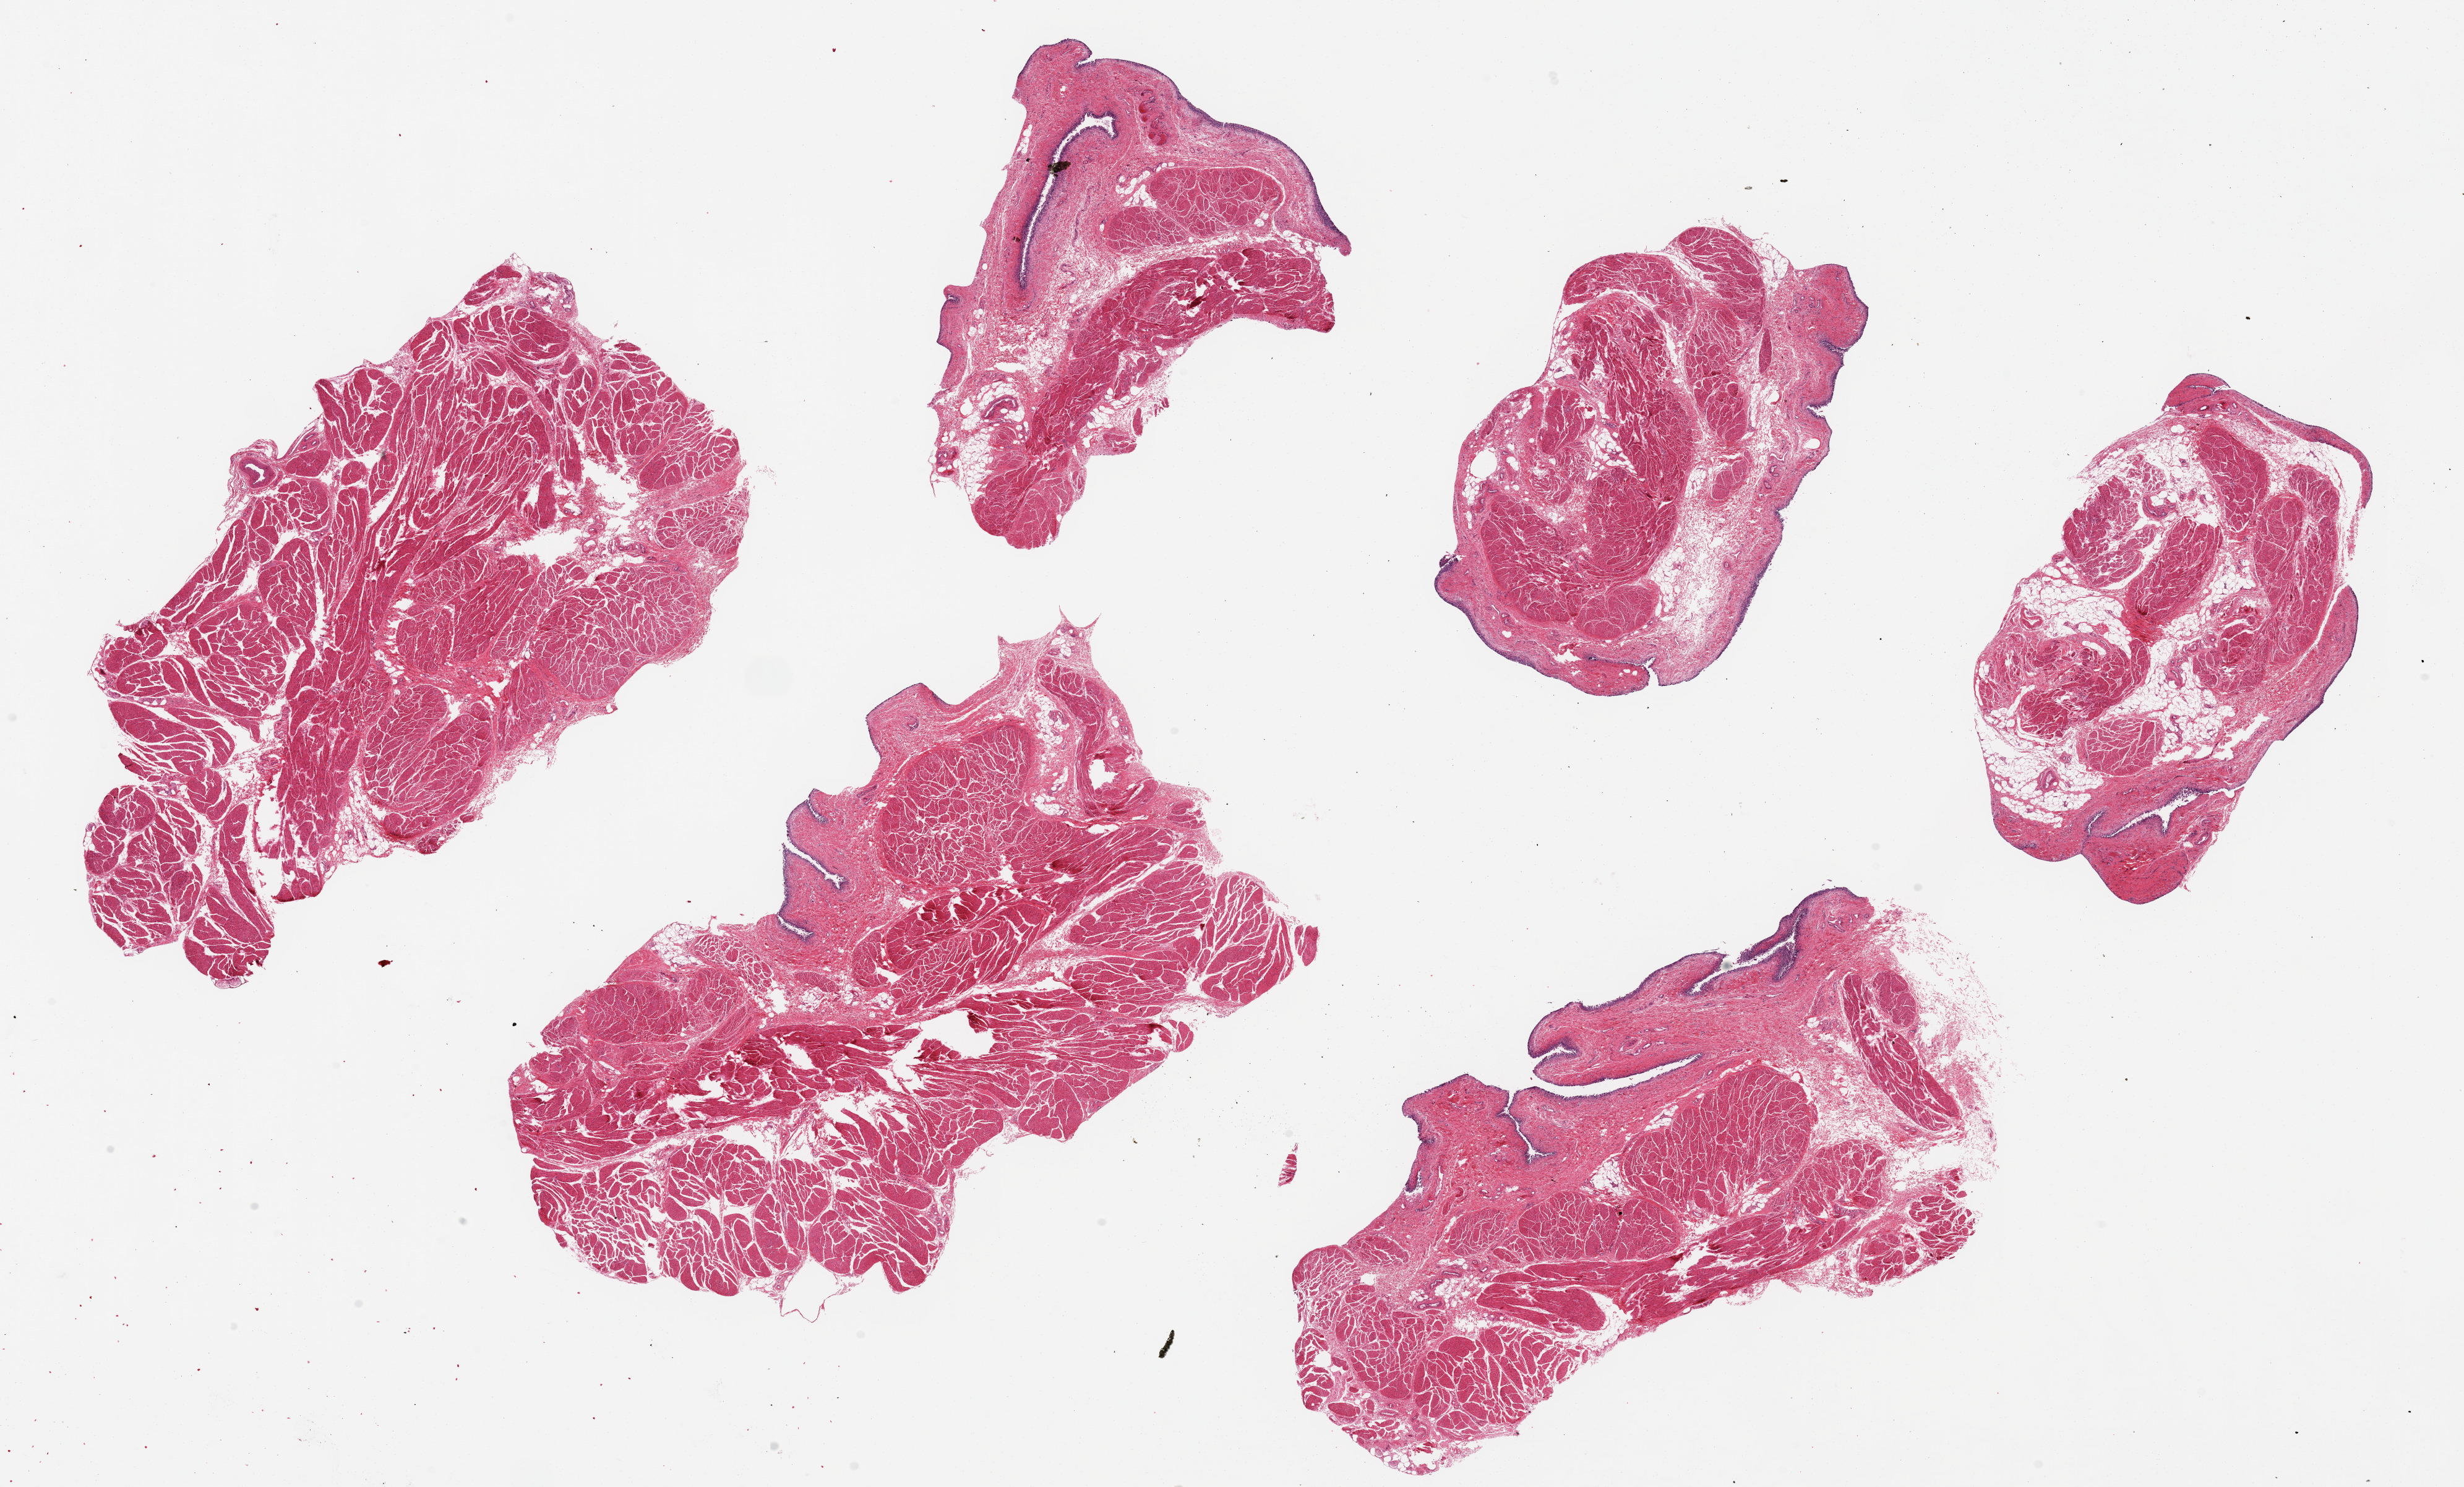
Hematoxylin and eosin (H&E) whole-slide image — low-resolution overview of the scanned area, about 31.5 x 19.0 mm (slide scanned at 20x), PAXgene-fixed paraffin-embedded (PFPE) section, section of urinary bladder (target tissue), tissue donor sample. Donor: male.
Review note (as recorded): 6 pieces up to 10x5.6 mm; epithelium largely sloughed.